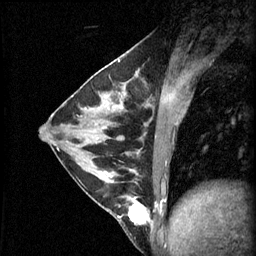
Breast MRI (dynamic contrast-enhanced), one sagittal slice. Position 24 of 60 along the scan axis. 3 images stored at this slice position (order not interpretable as contrast timing). 1.5 T. TE 4.2 ms, TR 11 ms. 2.1 mm slice thickness. 256 × 256 image matrix. Female patient, age 29 years.
Annotated regions visible in this slice (semi-automatically segmented with operator editing):
- analysis volume of interest (the breast-tissue region the enhancement analysis was run in; not a lesion): bounding box <93,164,153,229> (left, top, right, bottom; pixels)
- tumour enhancement mask (voxels above the 70 % enhancement threshold inside the analysis volume of interest): <117,196,153,227>